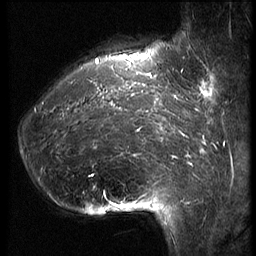
Breast MRI (dynamic contrast-enhanced), one sagittal slice; slice 15 of 62 in the series (ordered by position); 3 images stored at this slice position (order not interpretable as contrast timing); 1.5 T; TE 4.2 ms, TR 9 ms; 256 × 256 image matrix, field of view 180 × 180 mm. Patient: female, 39 years. From the clinical record (not read from this slice): setting: breast cancer imaged before/during neoadjuvant chemotherapy; receptor status: HER2-positive.
Annotated regions visible in this slice (semi-automatic segmentation, software-assisted and operator-edited):
- analysis volume of interest (the breast-tissue region the enhancement analysis was run in; not a lesion): bounding box <20,64,171,228> (left, top, right, bottom; pixels)
- tumour enhancement mask (voxels above the 140 % enhancement threshold inside the analysis volume of interest): <79,82,164,203>